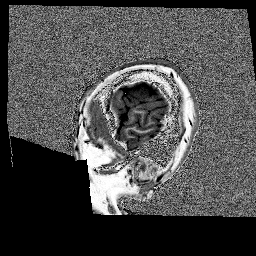
Brain MRI from a brain-tumour surgery series, one sagittal slice; slice 26 of 176 in the series (ordered by position); 1 mm slice thickness; 256 × 256 image matrix, field of view 256 × 256 mm. From the clinical record (not read from this slice): histopathology: Glioblastoma; WHO grade: 4; IDH mutation: no.
Annotated regions visible in this slice (outlined manually by an expert reader):
- tumour: bounding box [x1, y1, x2, y2] px = [118, 82, 175, 98]